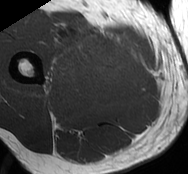
MRI of an extremity soft-tissue mass, one axial slice. MR volume resampled by the dataset authors to the PET/CT grid (not the native acquisition matrix). 3.27 mm slice thickness. 188 × 174 image matrix. Male patient. From the clinical record (not read from this slice): histological type: undifferentiated - pleiomorphic; grade: high; site of the primary tumour: right thigh.
Outlined on this slice (expert contour drawn on MRI and transferred to this co-registered scan by the dataset authors):
- gross tumour volume including surrounding oedema: bounding box (x1, y1, x2, y2) in pixels: (45, 26, 130, 88)
- gross tumour volume (mass): (91, 42, 130, 75)